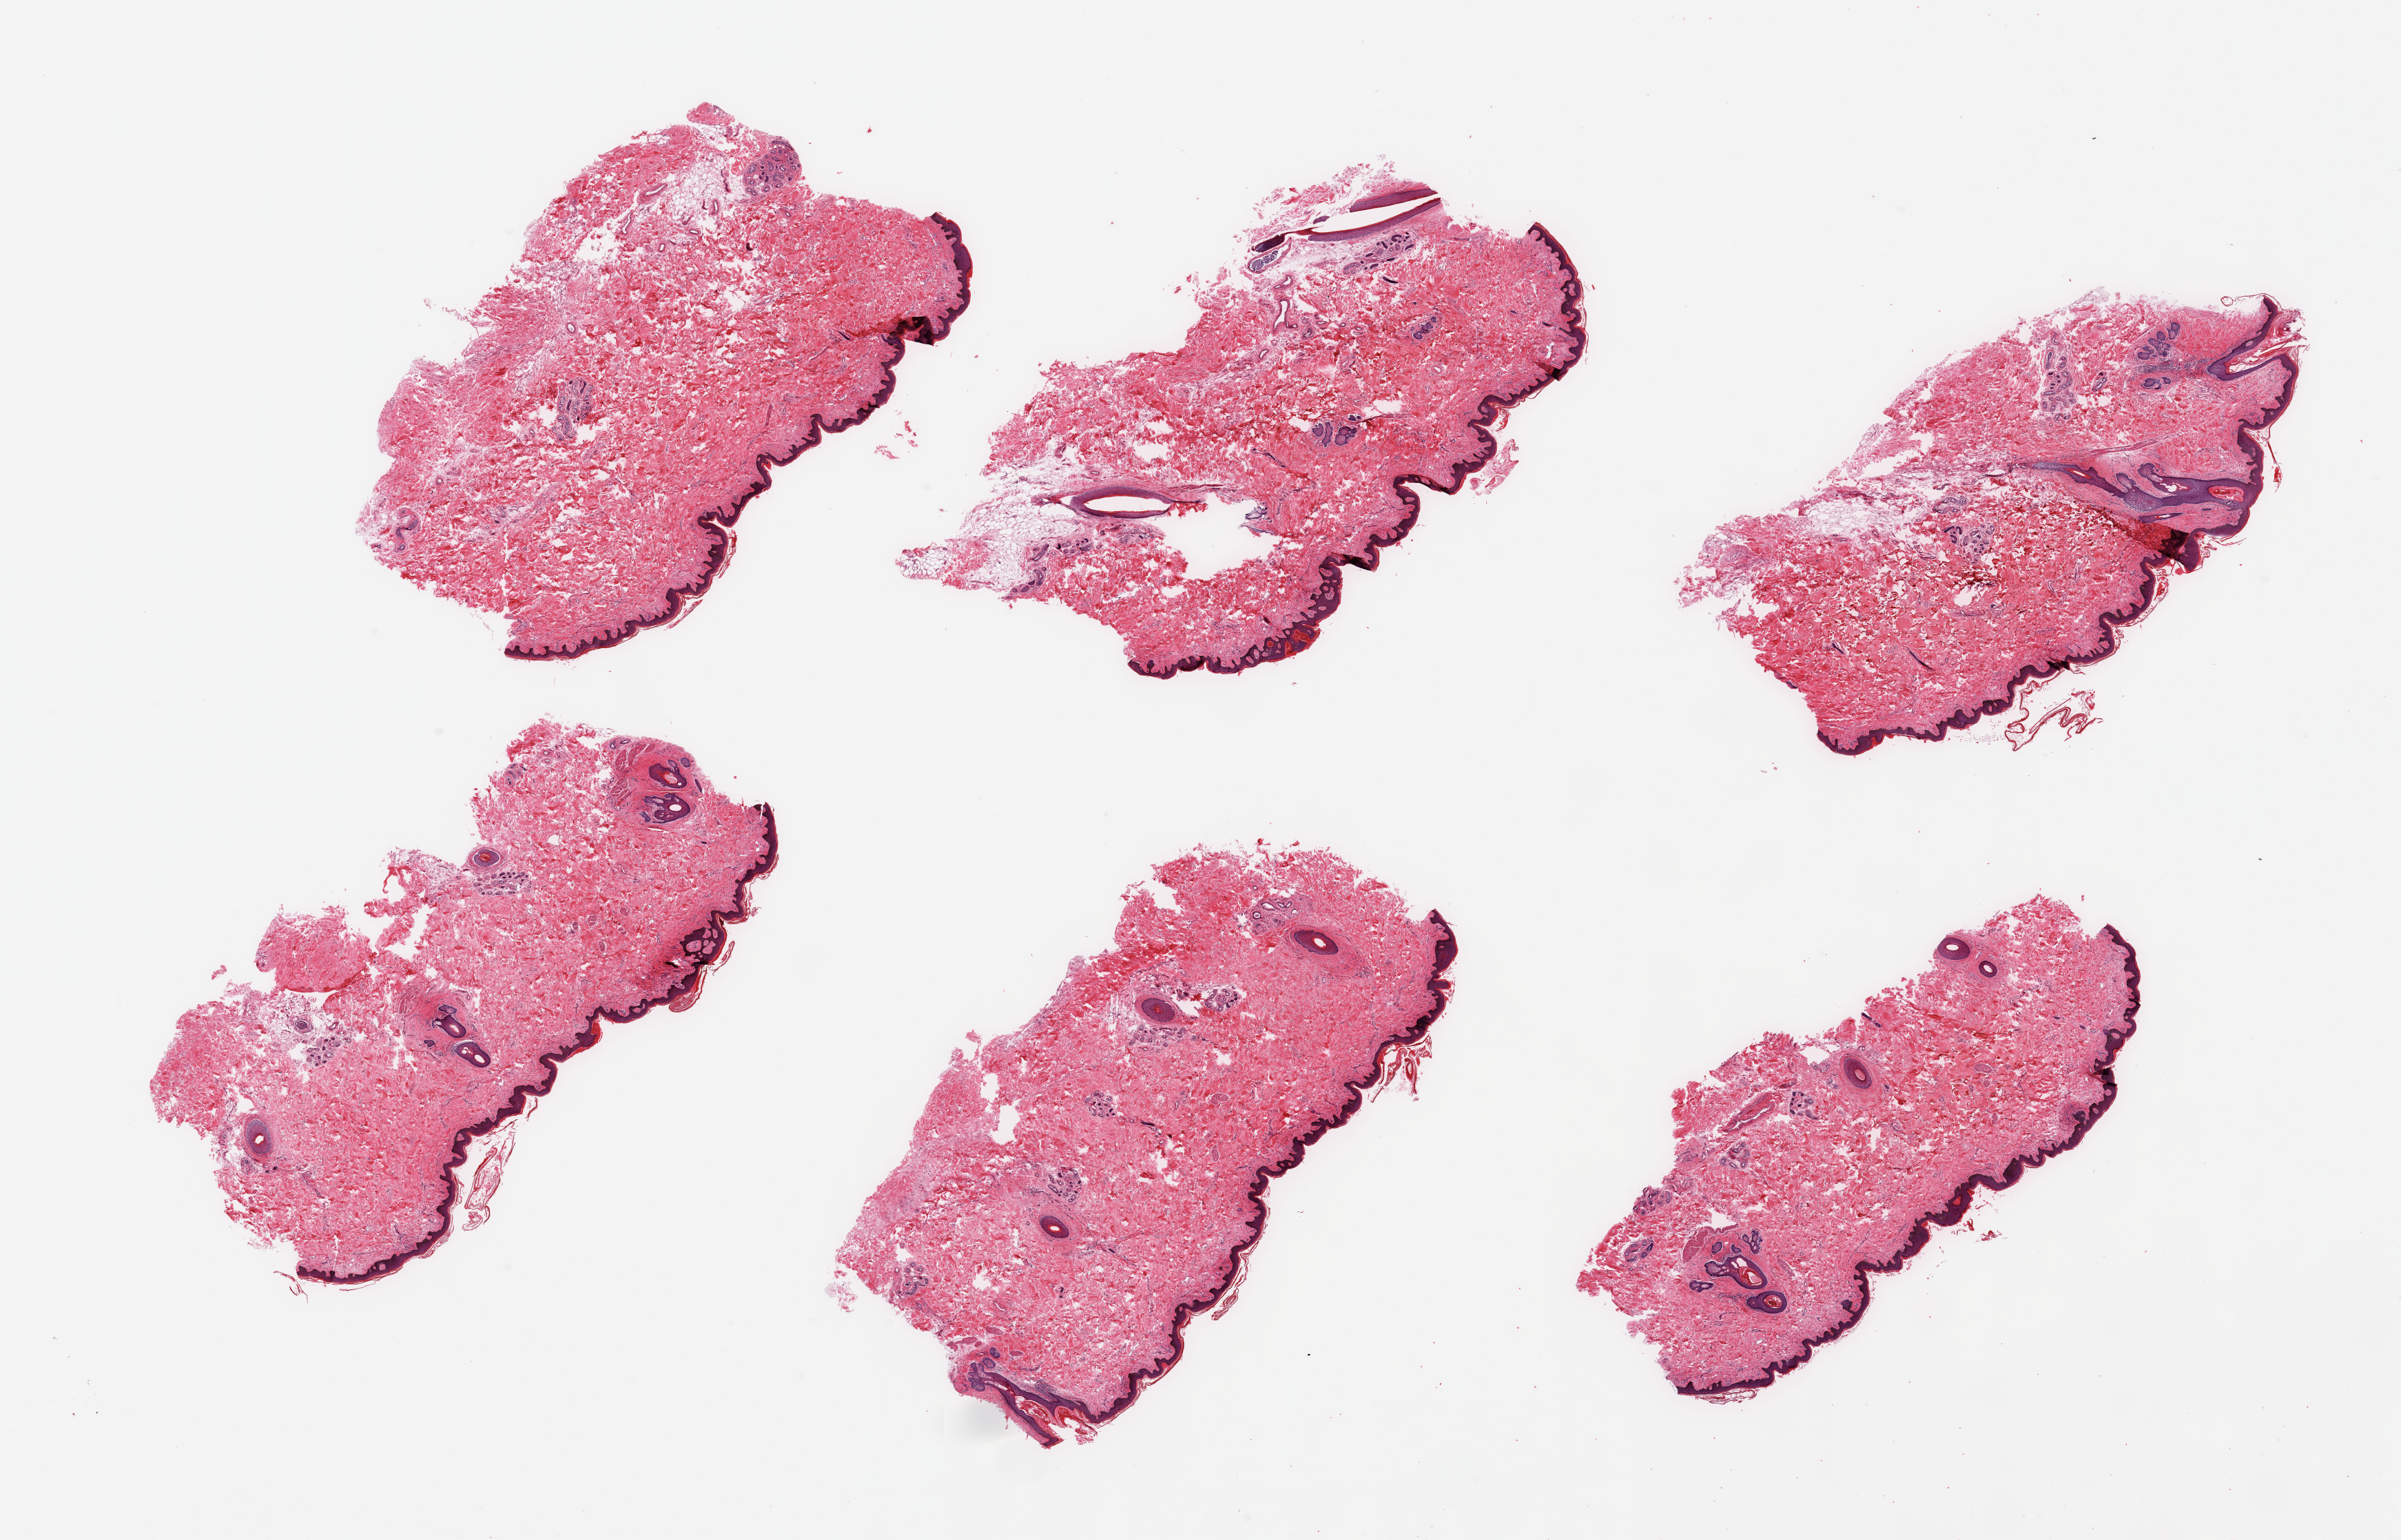
Whole-slide image, hematoxylin and eosin (H&E) stain, whole scanned area (about 27.6 x 17.7 mm) shown as a low-resolution overview; PAXgene-fixed paraffin-embedded (PFPE) section; section of skin of suprapubic region (target tissue); donor tissue sample. Donor: male.
* reviewer comment on this tissue sample: 6 pieces; insignificant internal/external fat